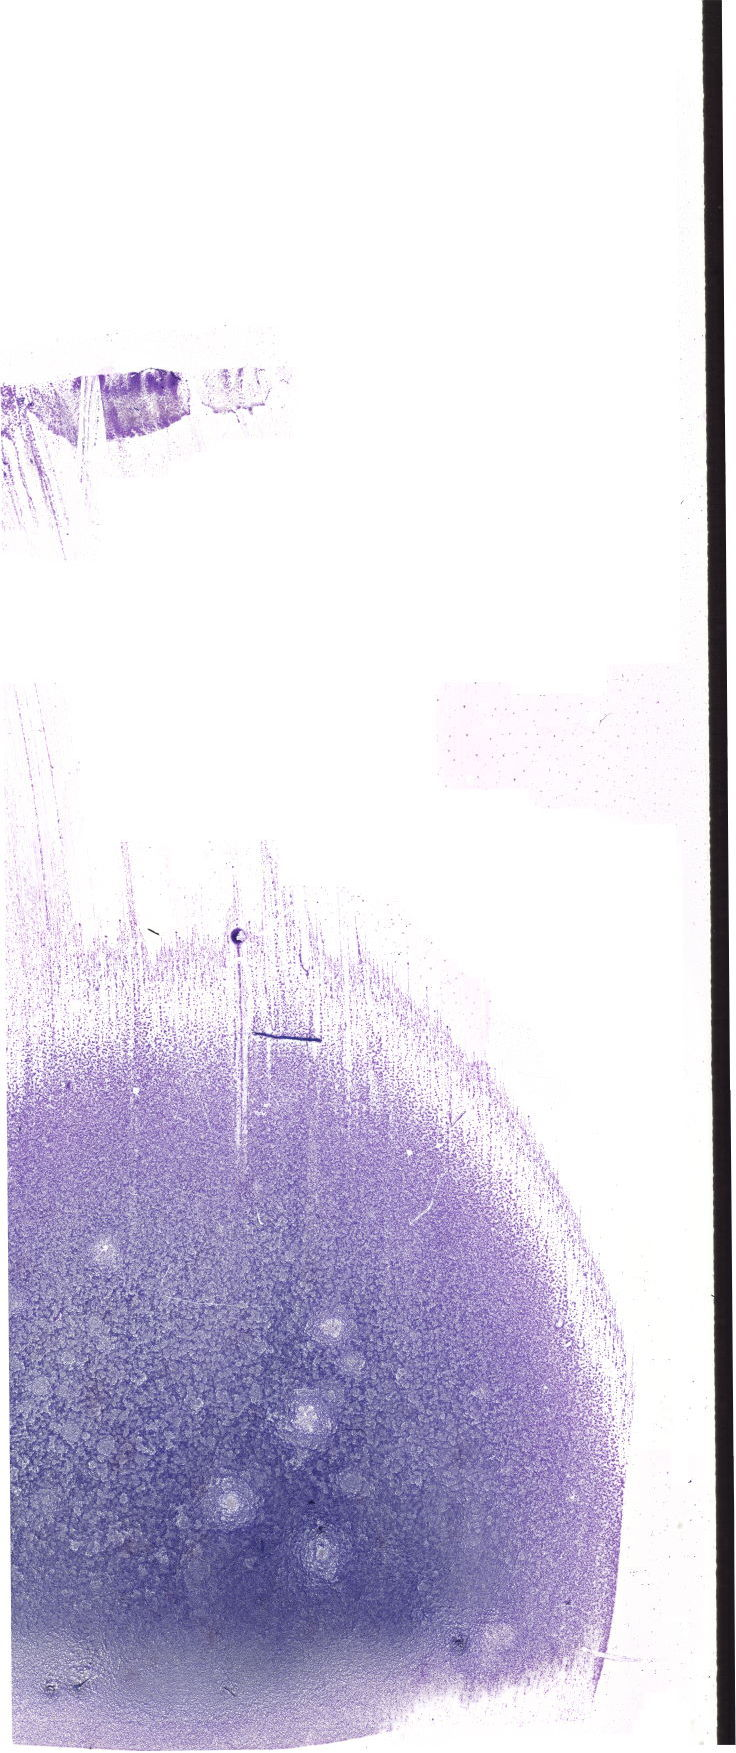
Bone marrow aspirate smear, May-Grünwald–Giemsa stain, whole-slide image, a low-resolution overview of the entire scanned area, about 20.9 x 49.7 mm. Male patient.
* diagnosis: Chronic Phase Chronic Myeloid Leukemia, BCR-ABL1 Positive